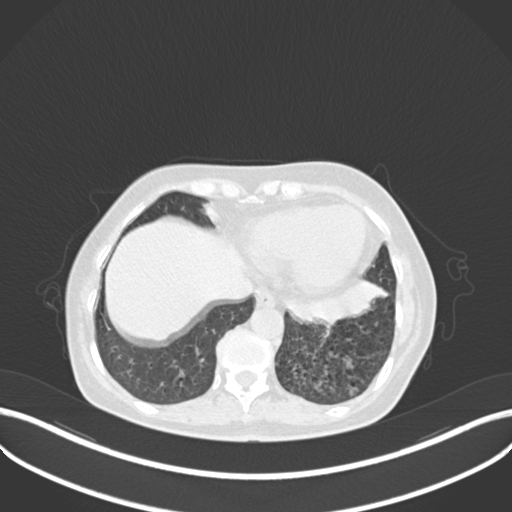
Chest CT, one axial slice; slice 61 of 270 in the series (ordered by position); 120 kVp; lung window (W 1500 / L -600 HU); 512 × 512 image matrix, field of view 400 × 400 mm. Patient: female, 63 years. From the clinical record (not read from this slice): clinical TNM (as recorded): T1b N0 M0.
Annotated regions visible in this slice (rectangle marked by the reading radiologist):
- lung tumour (recorded histology: adenocarcinoma): box from (x=281, y=280) to (x=394, y=330) px